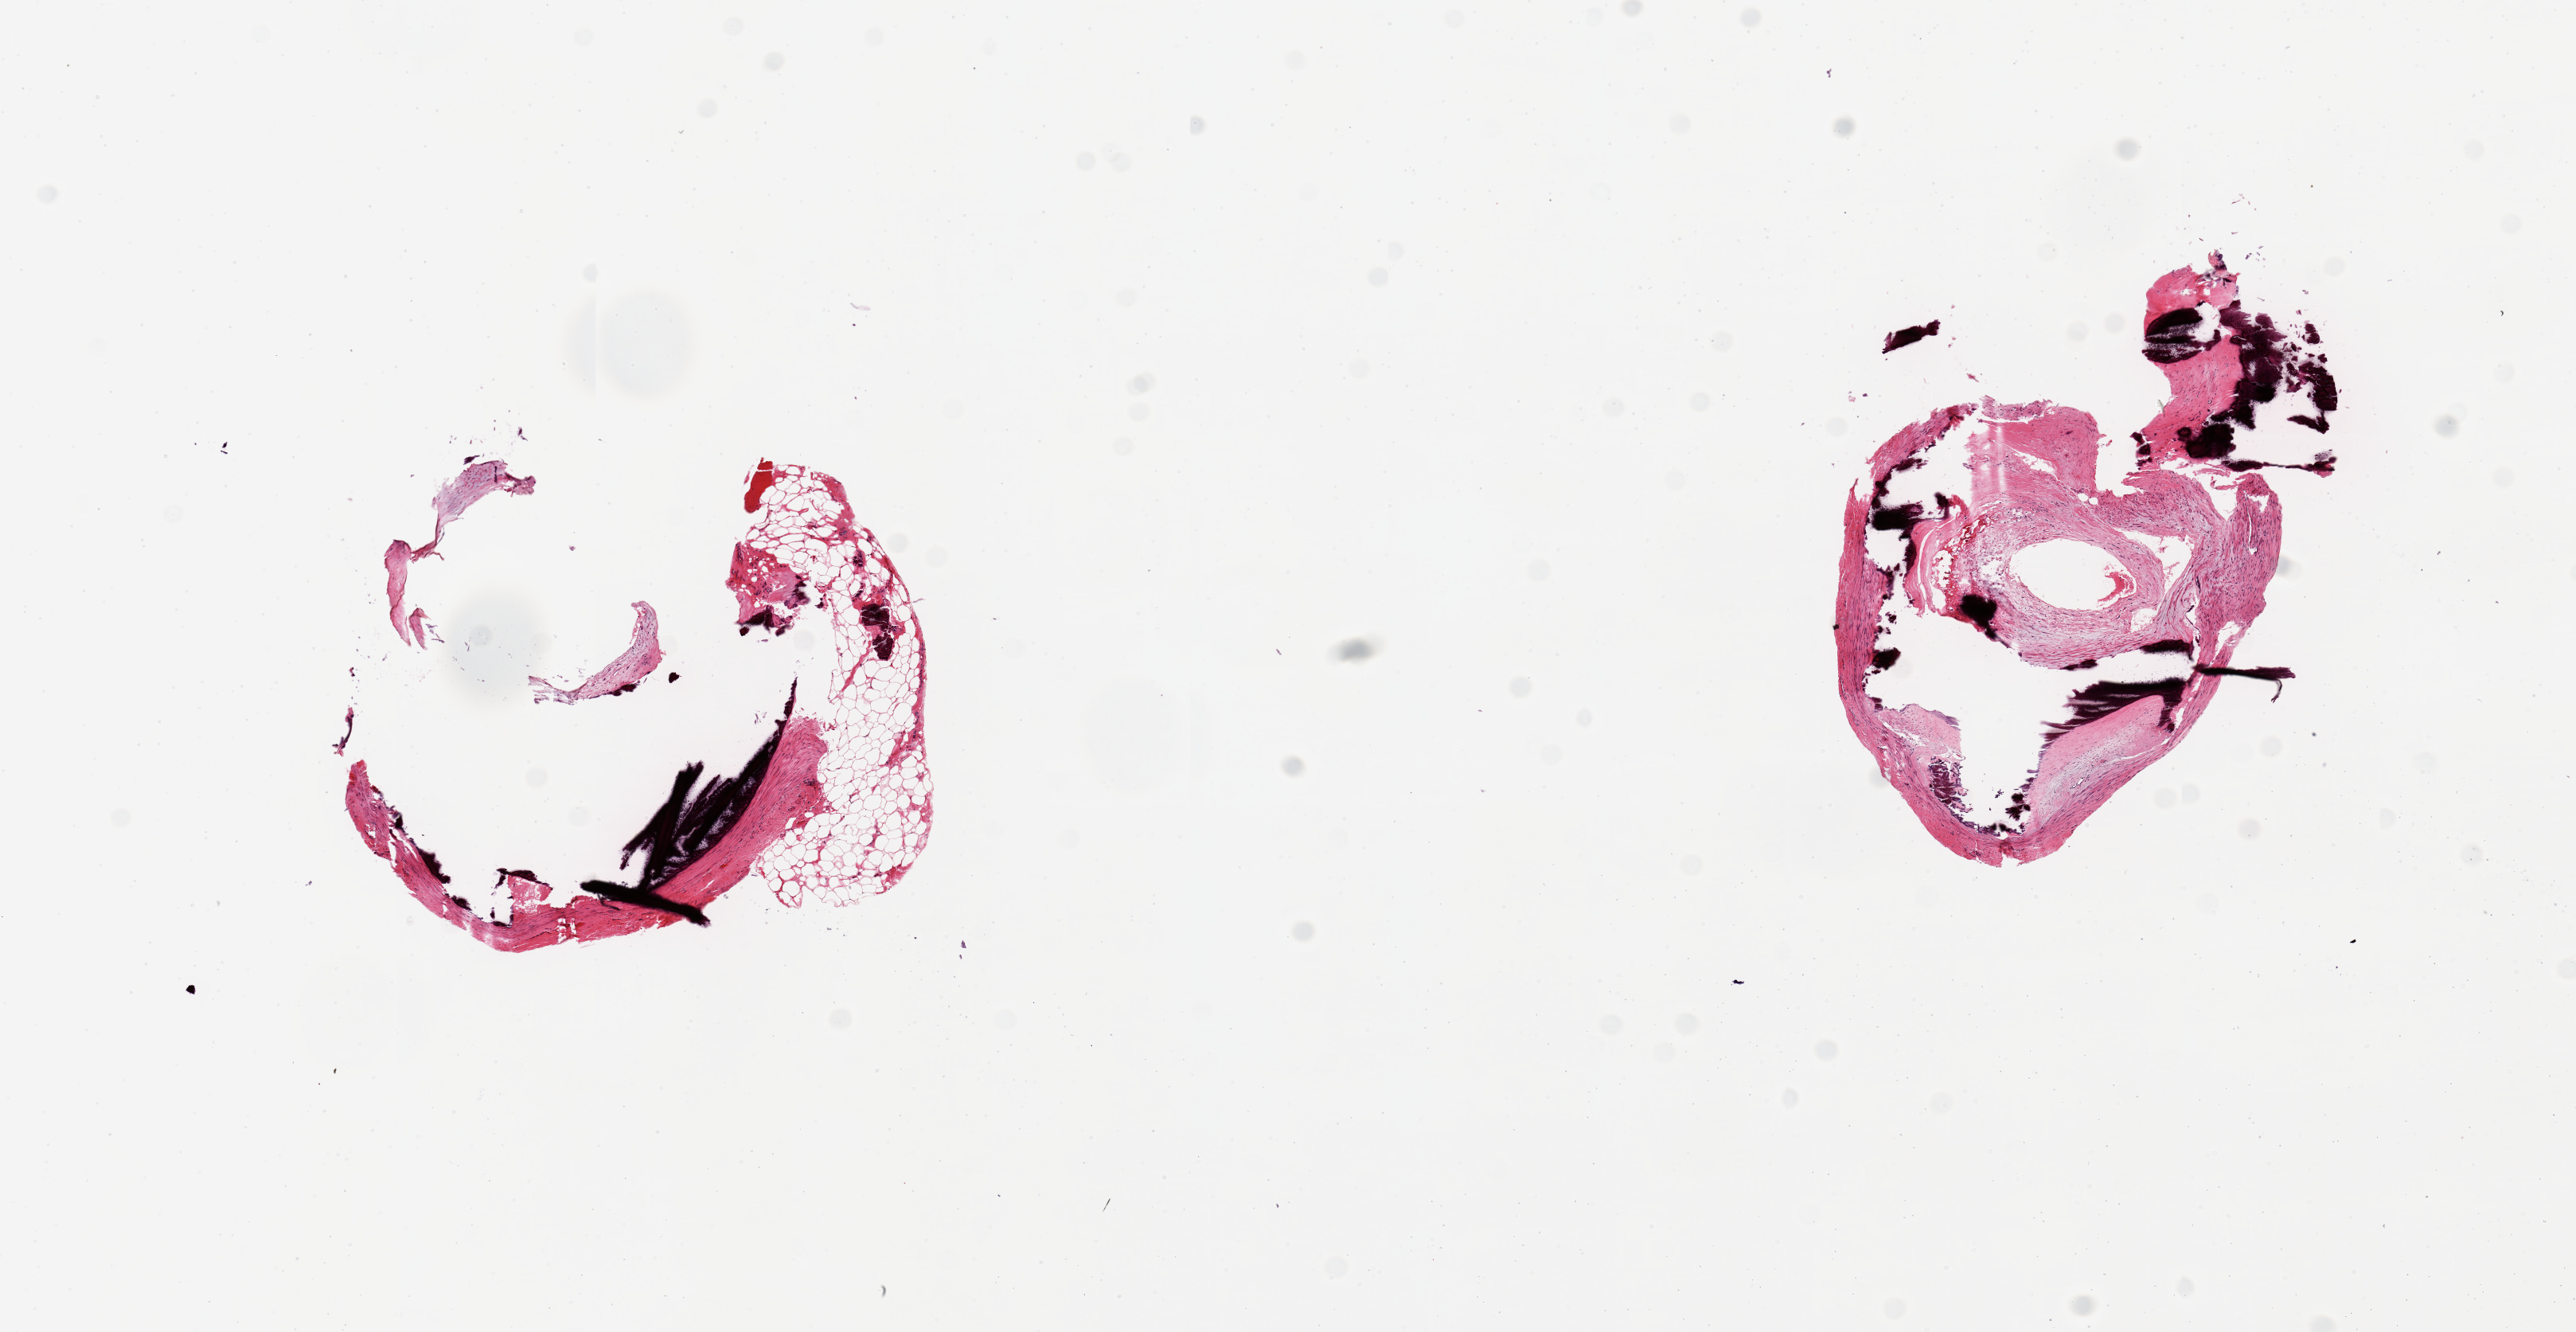
Whole-slide image, H&E stain — low-resolution overview of the scanned area, about 12.8 x 6.6 mm, PAXgene-fixed paraffin-embedded (PFPE) section, section of tibial artery (target tissue), donor tissue sample.
• pathologist's review note for this sample: 2 pieces, 3x3 & 3x2mm; Heavily calcified sclerotic plaques. Hardly any normal tissue. Lumen 0.6mm. One piece has 30% adipose. Lots of empty space where calcified tissue has dropped out